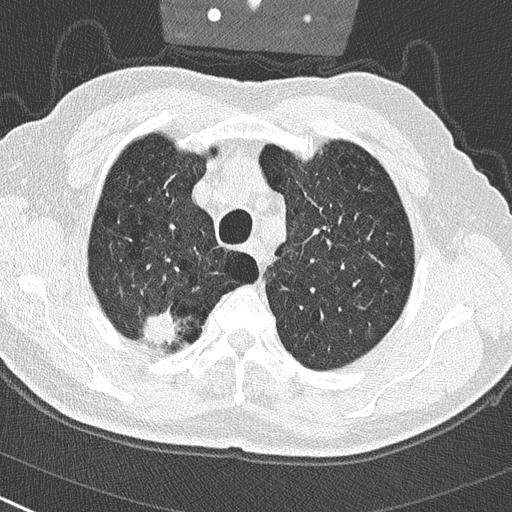
Low-dose screening chest CT, one axial slice. Position 236 of 290 along the scan axis. Reconstruction kernel B50f. Lung window (W 1500 / L -600 HU). 512 × 512 image matrix, field of view 300 × 300 mm.
Outlined on this slice (expert manual segmentation):
- lesion 1 (tumor, upper lobe of right lung): bounding box [x1, y1, x2, y2] px = [142, 312, 181, 349]